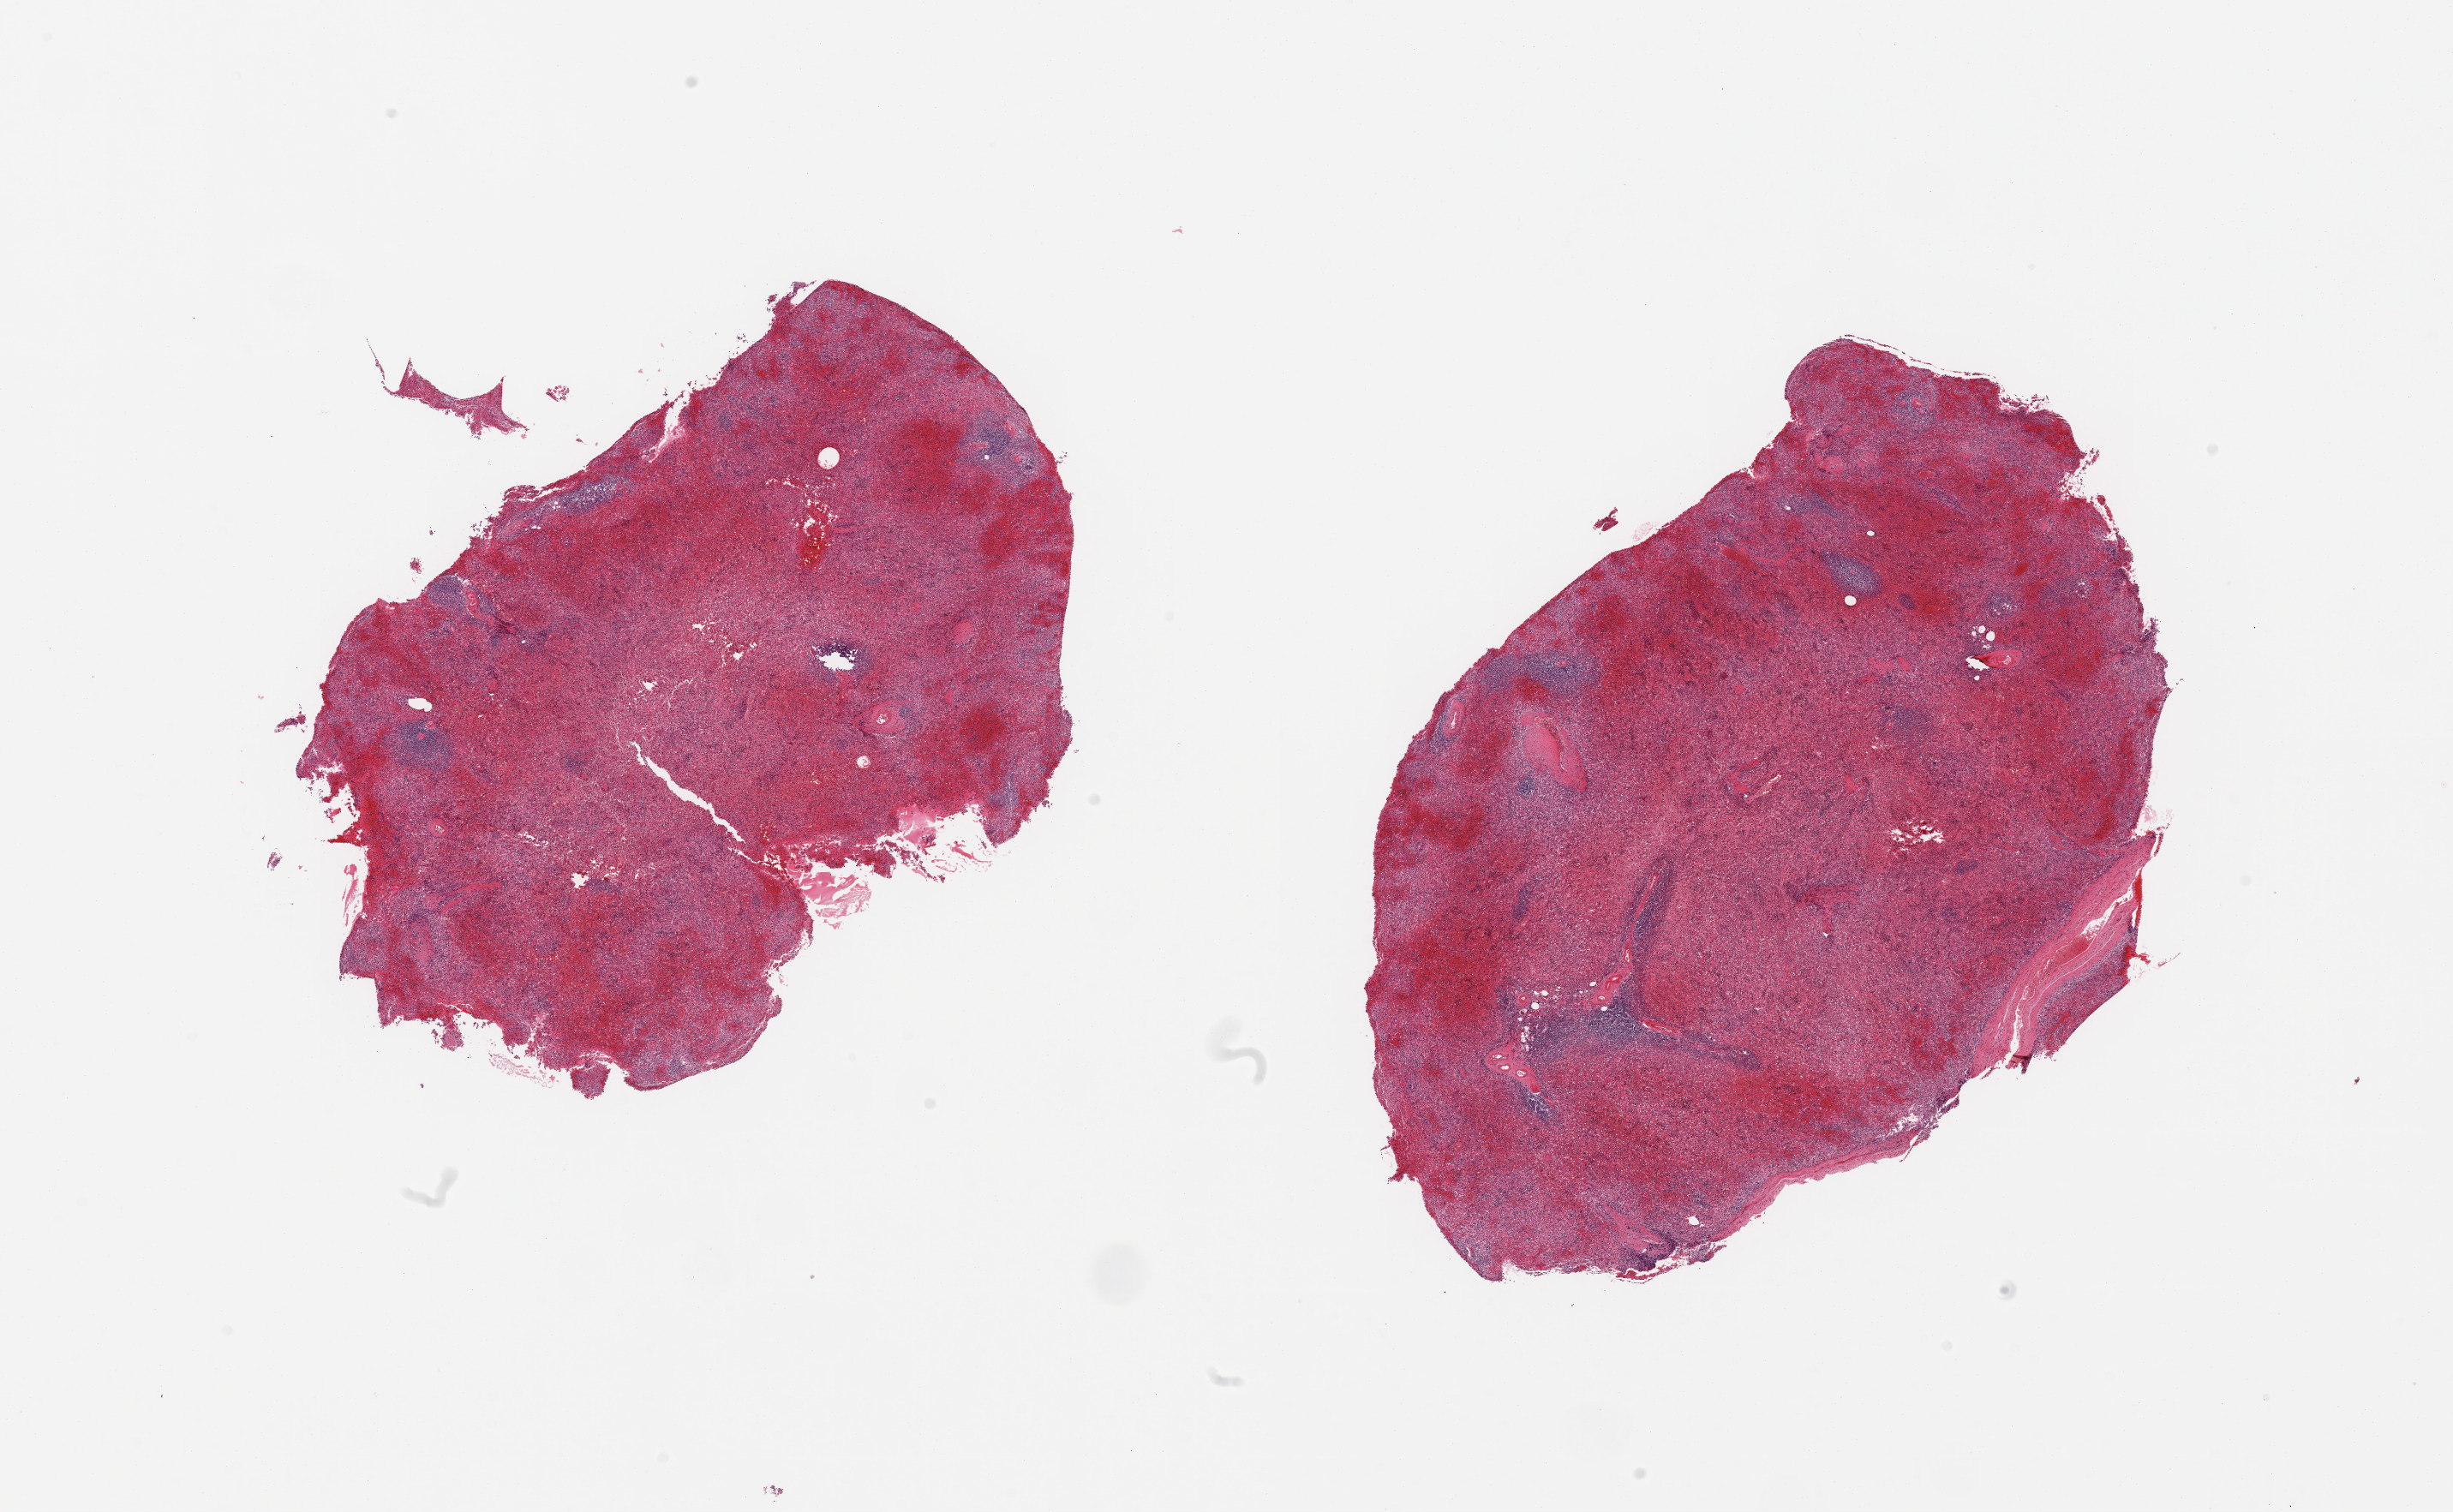
Whole-slide image, hematoxylin and eosin (H&E) stain — low-resolution overview of the scanned area, about 22.6 x 14.0 mm (slide scanned at 20x). PAXgene-fixed, paraffin-embedded tissue. Sampled site (target tissue): spleen. Tissue donor sample. Donor: male.
Pathologist's review note for this sample: 2 pieces; moderately congested.